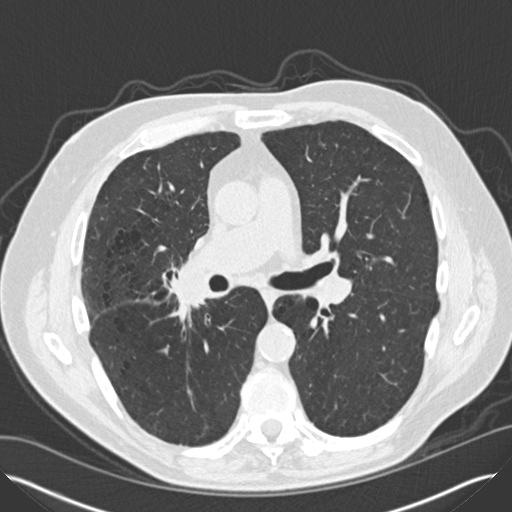
Low-dose screening chest CT, one axial slice. Slice 81 of 149 in the series (ordered by position). 120 kVp. Lung window (W 1500 / L -600 HU). 2 mm slice thickness. 512 × 512 image matrix.
Annotated regions visible in this slice (outlined manually by an expert reader):
- lesion 2 (tumor, hilum of right lung): box from (x=174, y=268) to (x=211, y=304) px